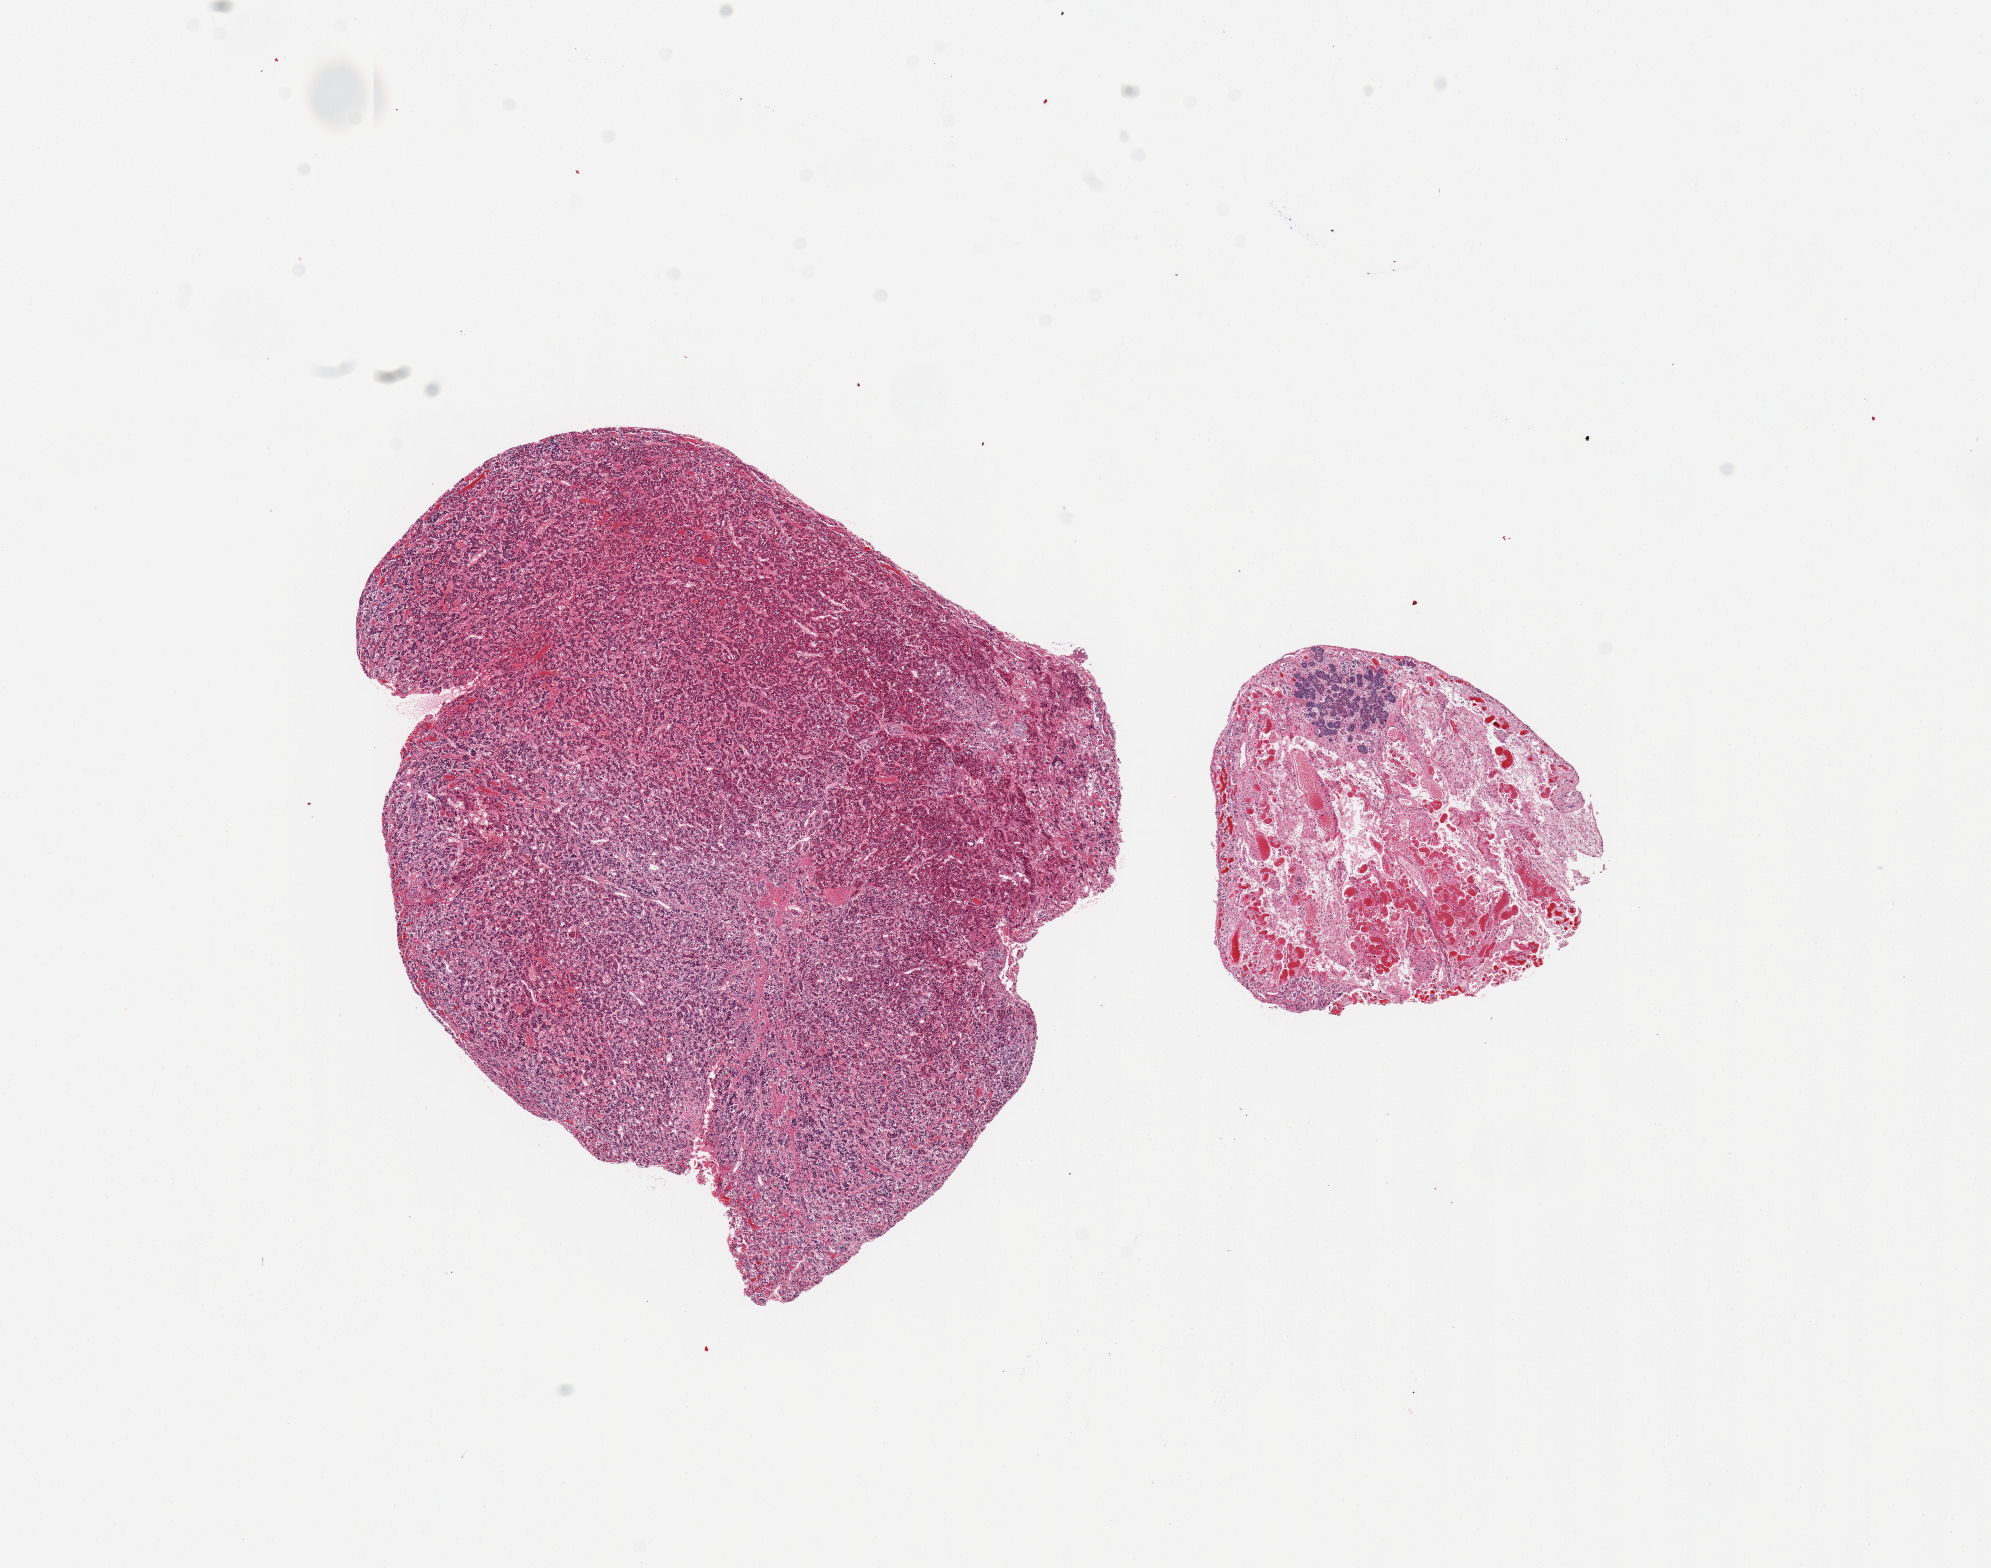
Hematoxylin and eosin (H&E) whole-slide image, a low-resolution overview of the entire scanned area, about 15.8 x 12.4 mm. PAXgene-fixed, paraffin-embedded tissue. Section of pituitary (target tissue). Tissue donor sample. Donor sex: female.
Reviewer comment on this tissue sample: 2 pieces, focus of squamous nests.